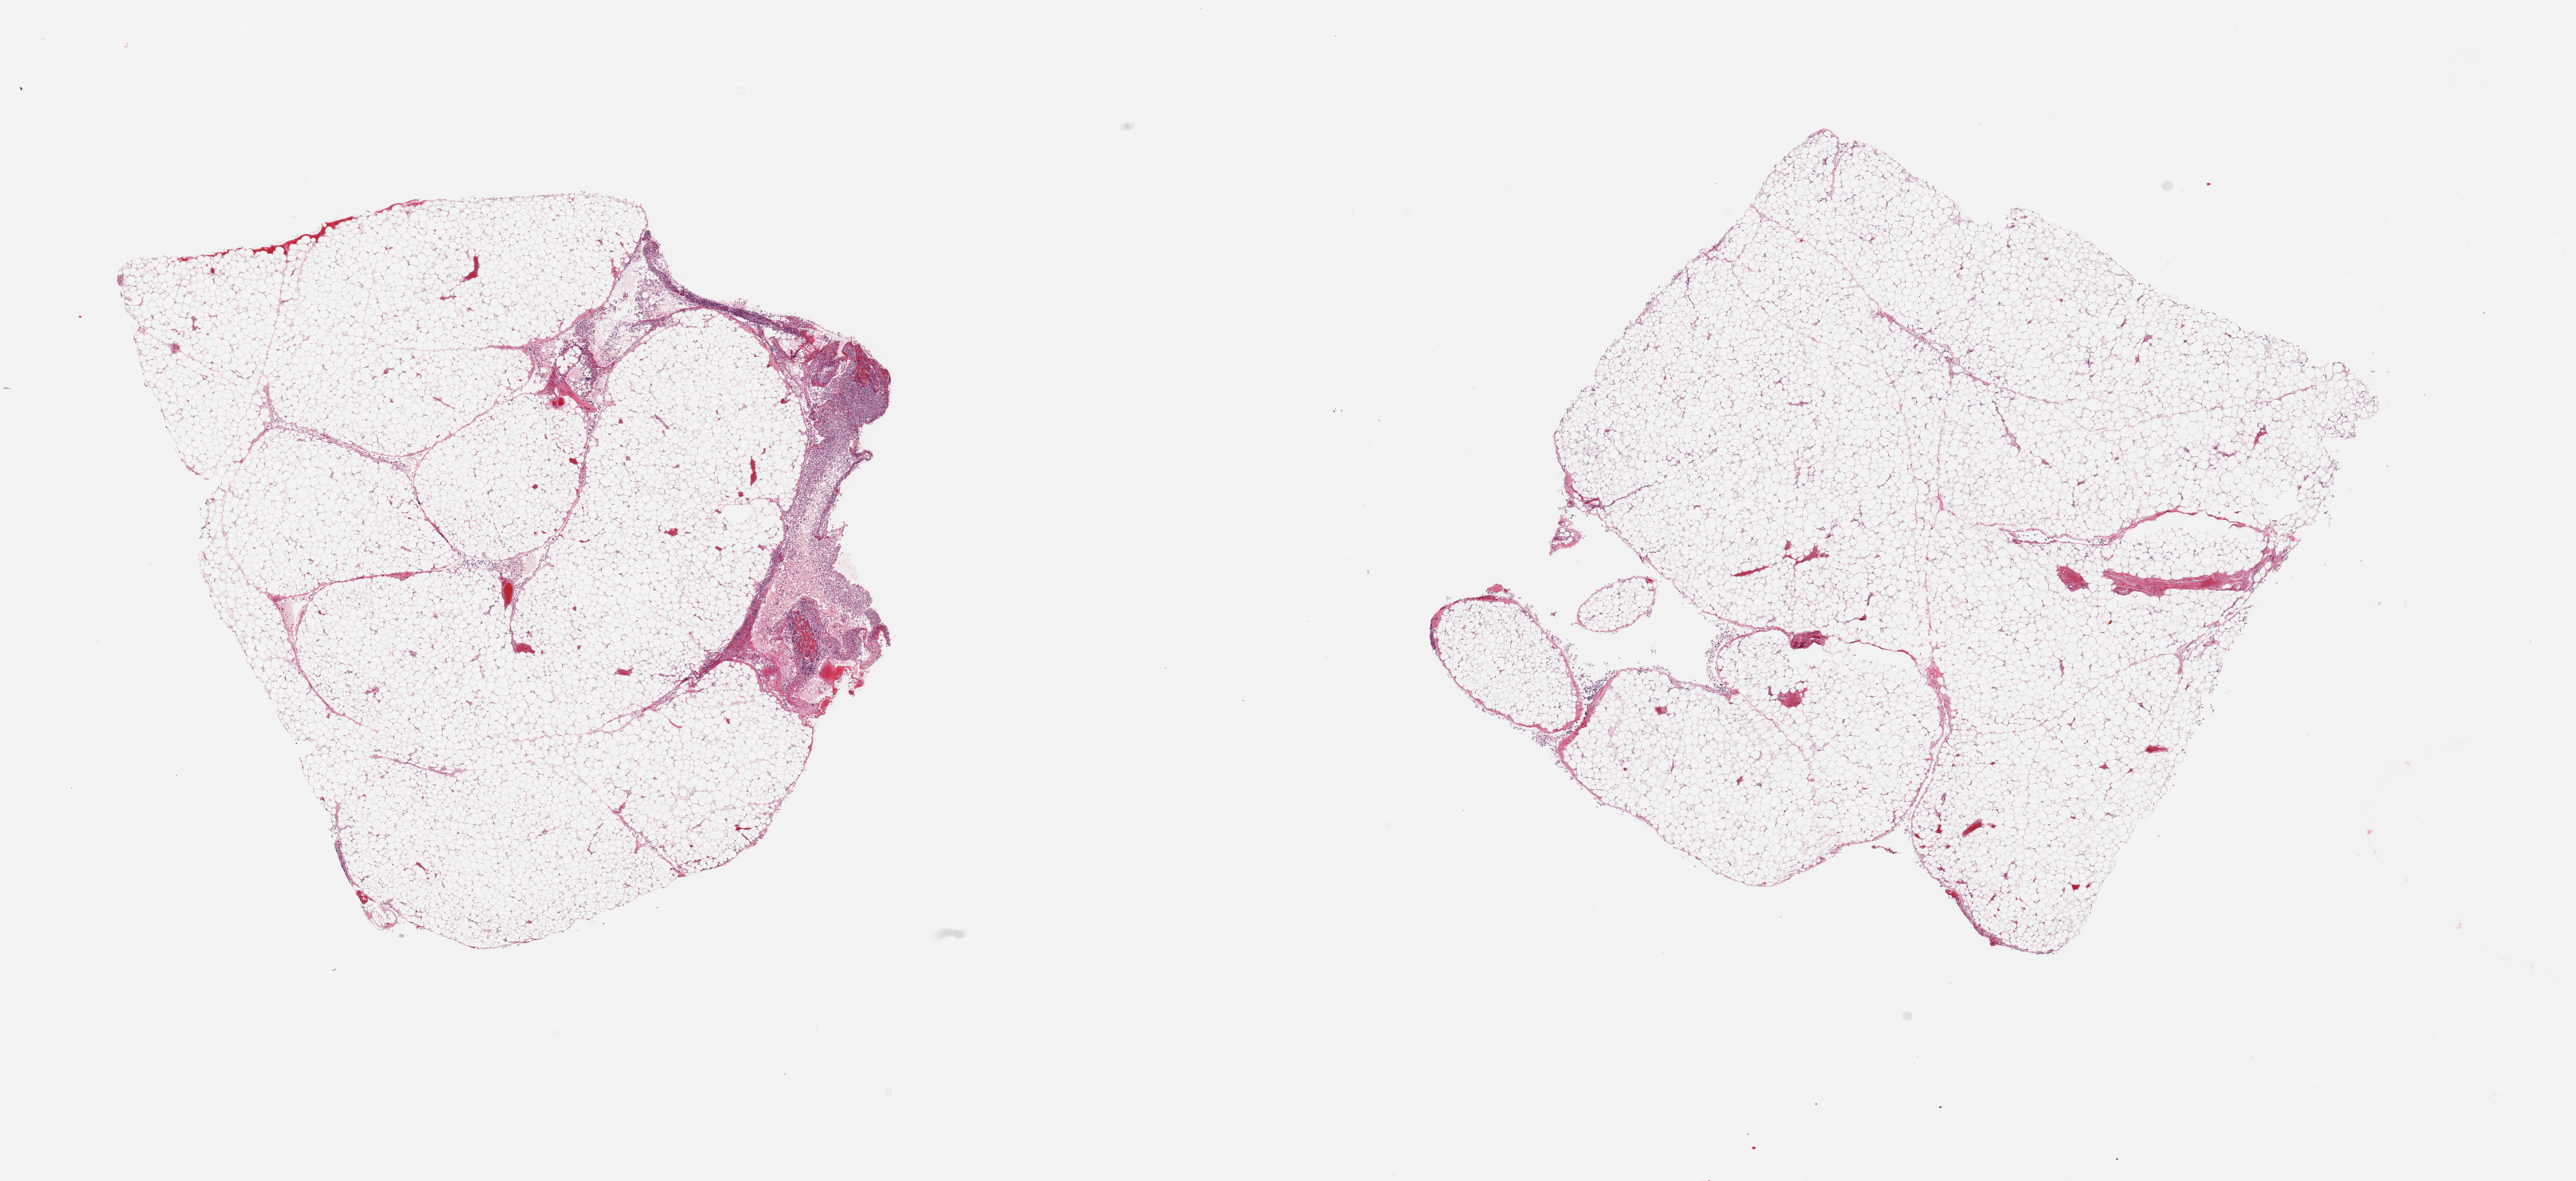
Digitized H&E-stained section, brightfield — low-resolution overview of the scanned area, about 25.6 x 11.7 mm, PAXgene-fixed paraffin-embedded (PFPE) section, section of omentum (target tissue), tissue donor sample. Donor: female.
Pathologist's review note for this sample: 2 pieces; polymorphs, mesothelial cells and fibrin on surface, especially on 1 piece, consistent with ascites (clinical history).